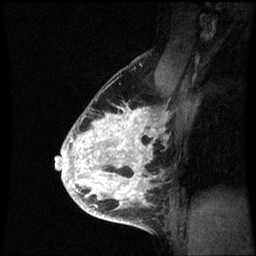
Breast MRI (dynamic contrast-enhanced), one sagittal slice. Position 45 of 60 along the scan axis. Dynamic contrast-enhanced series, image 2 of 3 at this slice position (ordered by acquisition). 1.5 T. TE 4.2 ms, TR 8.9 ms. 2 mm slice thickness. 256 × 256 image matrix, field of view 200 × 200 mm. Female patient, age 35 years. Case-level facts recorded for this patient, not image findings: setting: breast cancer imaged before/during neoadjuvant chemotherapy; receptor status: HR-positive, HER2-negative.
Outlined on this slice (semi-automatically segmented with operator editing):
- analysis volume of interest (the breast-tissue region the enhancement analysis was run in; not a lesion): bounding box <66,102,164,215> (left, top, right, bottom; pixels)
- tumour enhancement mask (voxels above the 70 % enhancement threshold inside the analysis volume of interest): <66,104,158,215>